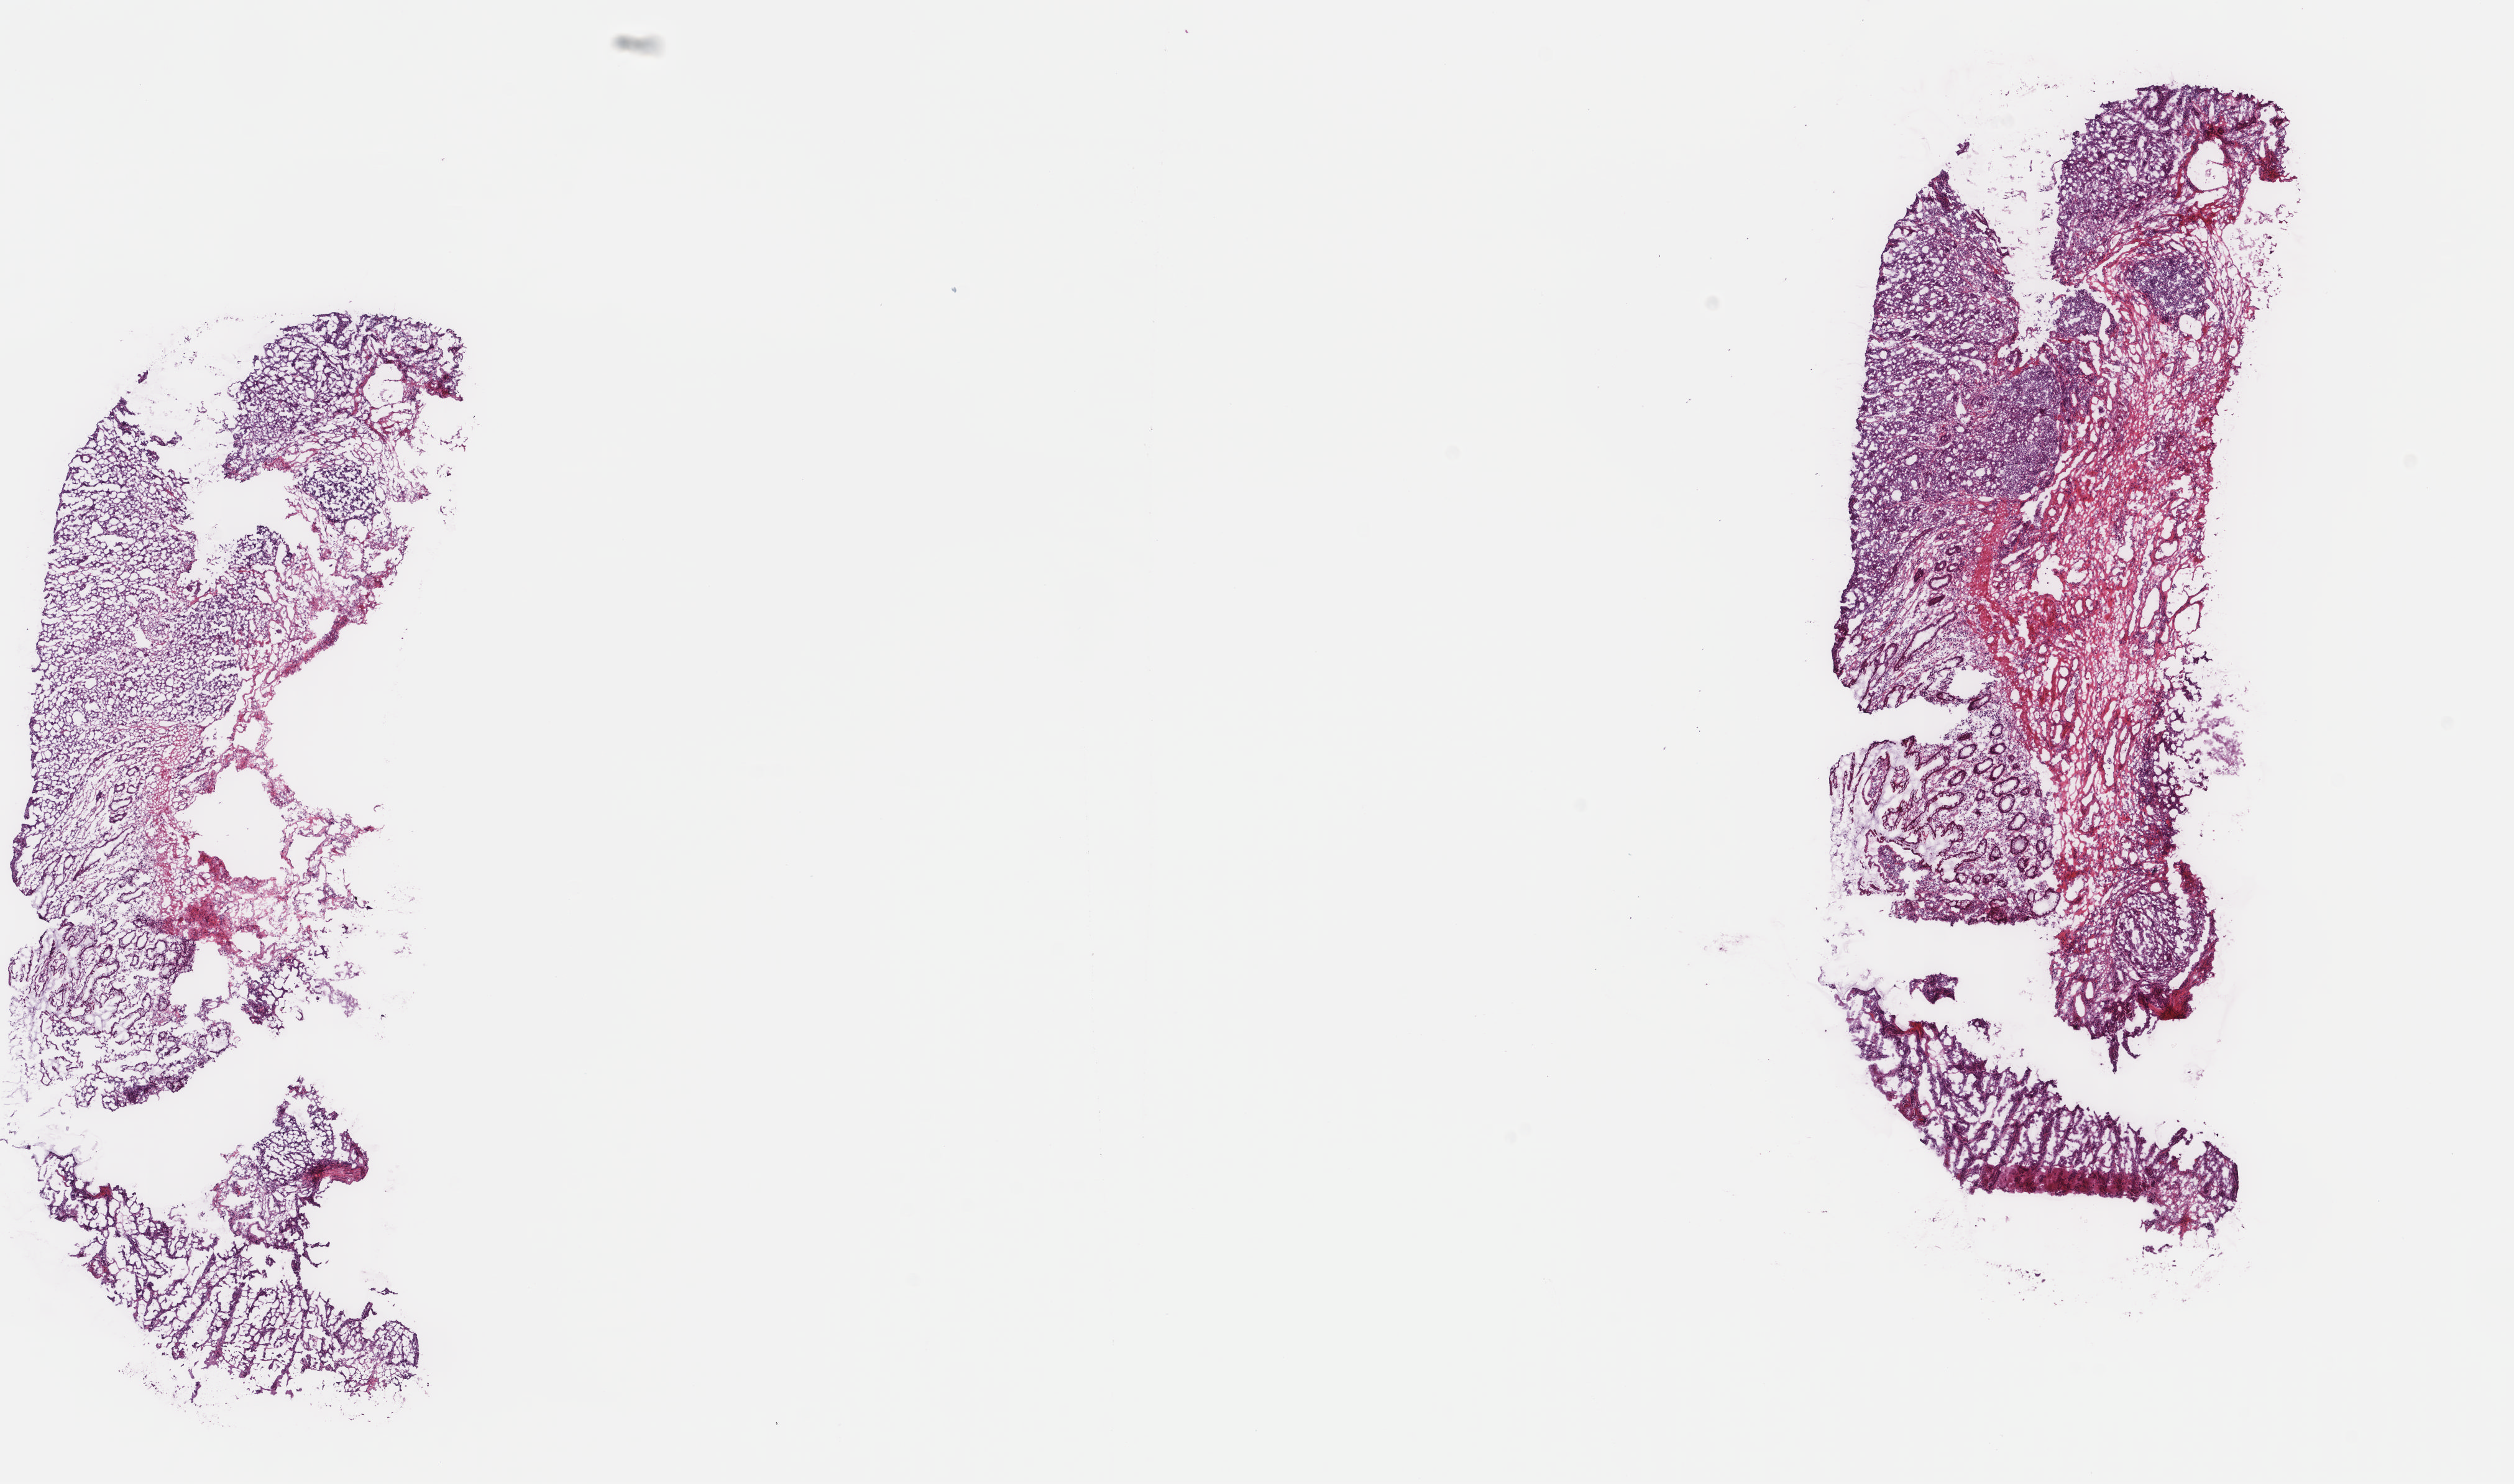
Digitized Hematoxylin and eosin (H&E) stained tissue section (whole slide) — a low-resolution overview of the entire scanned area, about 16.1 x 9.5 mm. Frozen section. Primary tumour sample from the colon. Patient: male, age at initial diagnosis 50 years. Pathologist review of this section (percent, as recorded): tumour cells 65%, tumour nuclei 65%, normal cells 8%, stromal cells 25%, necrosis 2%. Infiltration values recorded for this section: lymphocyte infiltration 4%, monocyte infiltration 1%, neutrophil infiltration 2%.
Lymph nodes positive (case pathology): 8 of 12 examined. Pathologic diagnosis: Adenocarcinoma, NOS. AJCC pathologic stage: IIIC (6th edition).